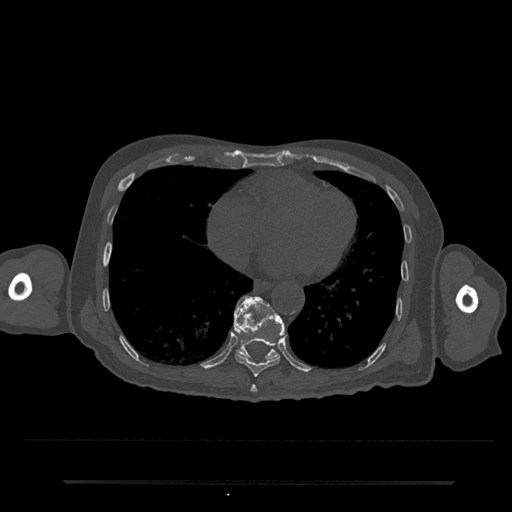
CT including the spine, one axial slice; position 348 of 797 along the scan axis; reconstruction kernel Br40s/3; bone window (W 1800 / L 400 HU); 0.5 mm slice thickness; 512 × 512 image matrix, field of view 427 × 427 mm. Male patient, age 74 years. From the clinical record (not read from this slice): primary cancer: prostate.
Annotated regions visible in this slice (semi-automatically segmented with operator editing):
- T10 vertebra: bounding box (x1, y1, x2, y2) in pixels: (234, 296, 285, 361)
- T8 vertebra: (250, 385, 258, 393)
- T9 vertebra: (234, 296, 285, 377)